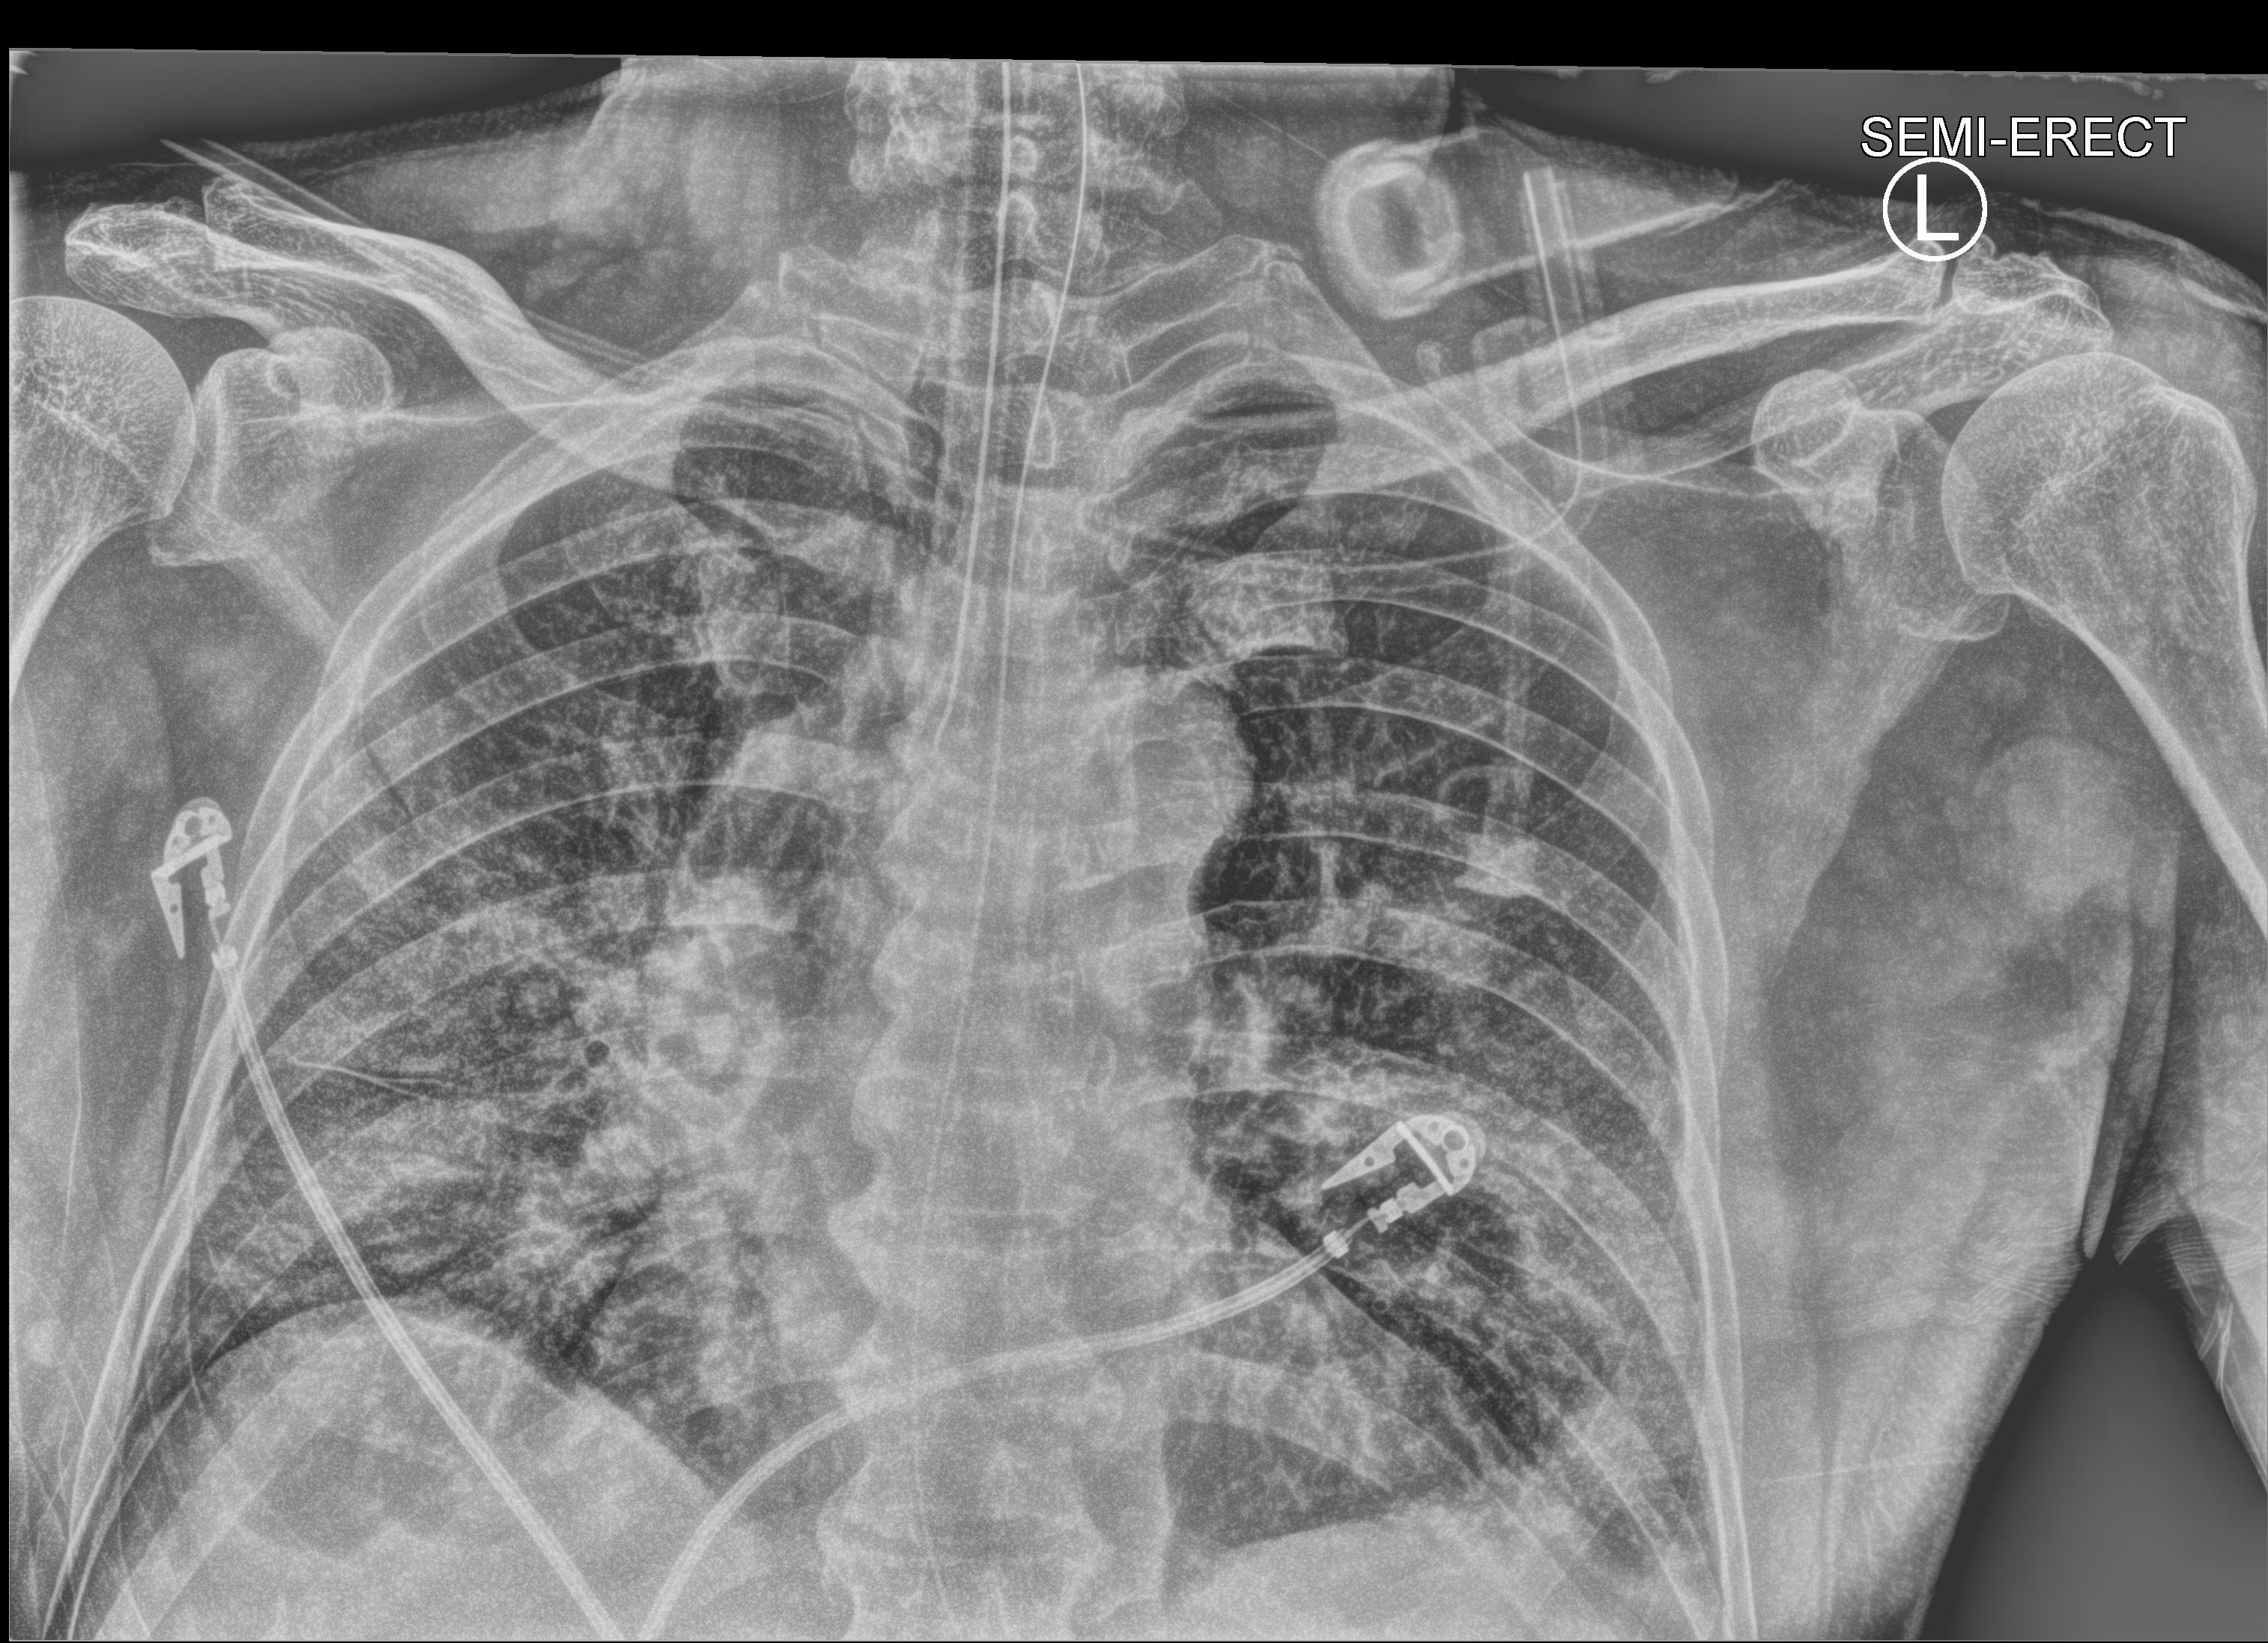
Portable chest radiograph. Male patient hospitalised with COVID-19, age 60–74 years.
Hospital-stay facts (about this admission, not read from this image; timing relative to this image not recorded): other chronic lung disease (admission record): no.